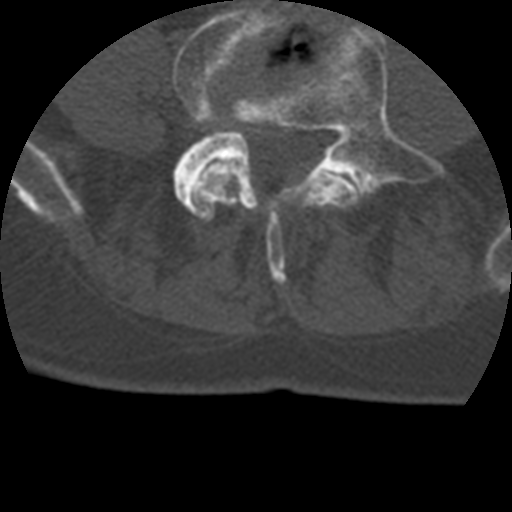
CT including the spine, one axial slice; position 53 of 399 along the scan axis; reconstruction kernel STANDARD; bone window (W 1800 / L 400 HU); 1.25 mm slice thickness; 512 × 512 image matrix, field of view 160 × 160 mm. Patient age 69 years. From the clinical record (not read from this slice): primary cancer: prostate.
Outlined on this slice (semi-automatically segmented with operator editing):
- L4 vertebra: bounding box <173,1,361,284> (left, top, right, bottom; pixels)
- L5 vertebra: <173,26,432,210>